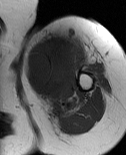
MRI of an extremity soft-tissue mass, one axial slice; slice 56 of 86 in the series (ordered by position); MR volume resampled by the dataset authors to the PET/CT grid (not the native acquisition matrix); 3.27 mm slice thickness; 126 × 155 image matrix. Female patient. Case-level facts recorded for this patient, not image findings: histological type: pleiomorphic leiomyosarcoma; grade: high; site of the primary tumour: left biceps.
Outlined on this slice (expert contour drawn on MRI and transferred to this co-registered scan by the dataset authors):
- gross tumour volume including surrounding oedema: bounding box <25,37,80,114> (left, top, right, bottom; pixels)
- gross tumour volume (mass): <25,37,78,98>